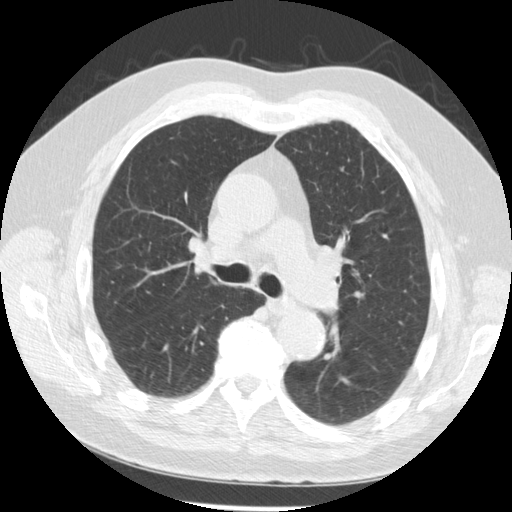
Low-dose screening chest CT, one axial slice; slice 166 of 259 in the series (ordered by position); reconstruction kernel STANDARD; lung window (W 1500 / L -600 HU); 2.5 mm slice thickness; 512 × 512 image matrix, field of view 355 × 355 mm.
Structures marked on this image (expert manual segmentation):
- lesion 2 (tumor, hilum of right lung): box from (x=194, y=245) to (x=212, y=270) px